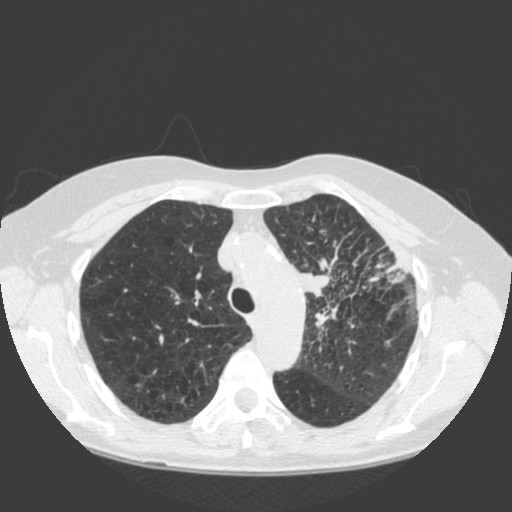
Low-dose screening chest CT, one axial slice; slice 141 of 184 in the series (ordered by position); lung window (W 1500 / L -600 HU); 2 mm slice thickness; 512 × 512 image matrix.
Annotated regions visible in this slice (expert manual segmentation):
- lesion 1 (tumor, hilum of left lung): bounding box (x1, y1, x2, y2) in pixels: (294, 268, 331, 296)